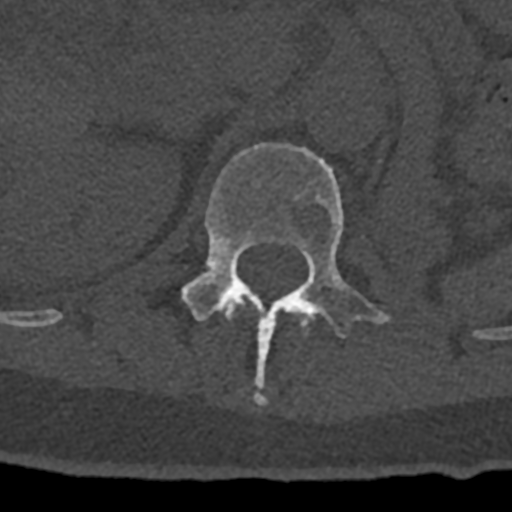
CT including the spine, one axial slice; slice 445 of 797 in the series (ordered by position); reconstruction kernel Br40s/3; 120 kVp; bone window (W 1800 / L 400 HU); 512 × 512 image matrix, field of view 160 × 160 mm. Patient: male, 74 years. Case-level facts recorded for this patient, not image findings: primary cancer: renal; vertebrae with lytic lesions (as recorded): T10, L1, L2, L3, L4, L5.
Outlined on this slice (semi-automatic segmentation, software-assisted and operator-edited):
- L1 vertebra: bounding box <182,143,392,405> (left, top, right, bottom; pixels)
- T12 vertebra: <221,297,313,335>